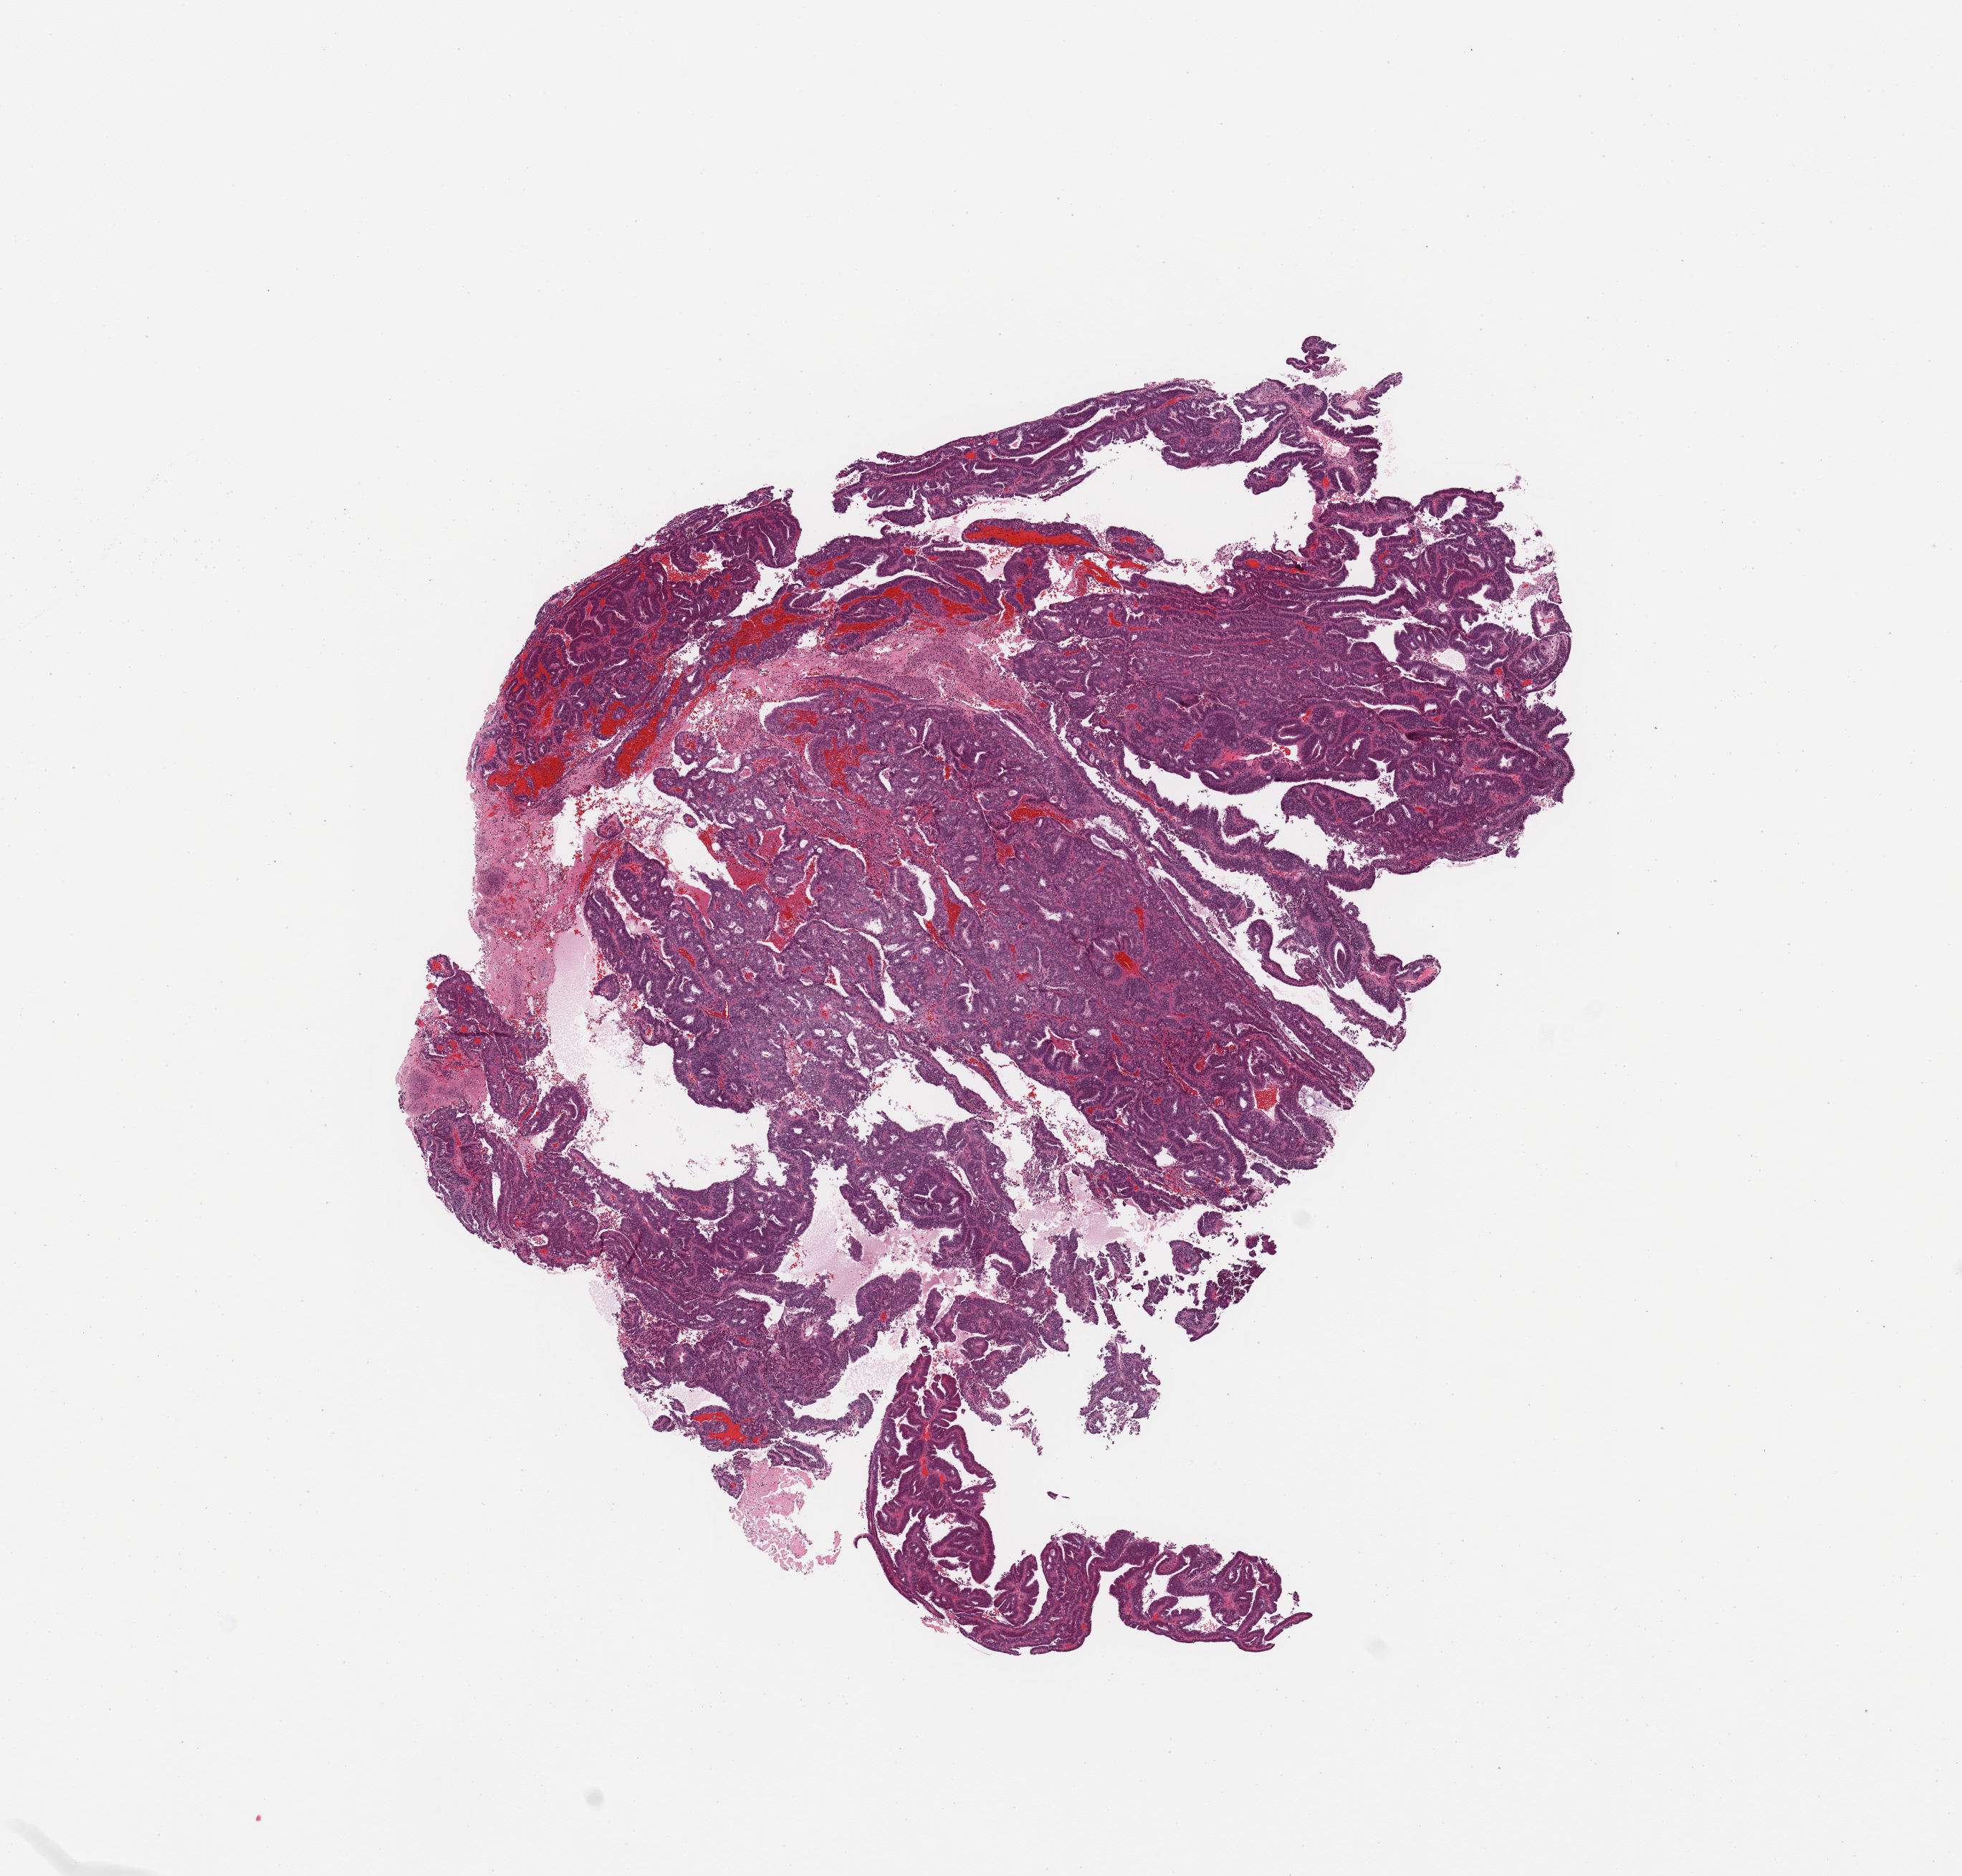
Digitized Hematoxylin and eosin (H&E) stained tissue section (whole slide), a low-resolution overview of the entire scanned area, about 10.8 x 10.4 mm (acquisition: 20x scan), tumour tissue sample, sampled site: uterus. 75-year-old female patient. Composition of this section per pathologist review: tumour nuclei 95%, necrosis 10%.
Histologic diagnosis: Endometrioid adenocarcinoma, NOS.